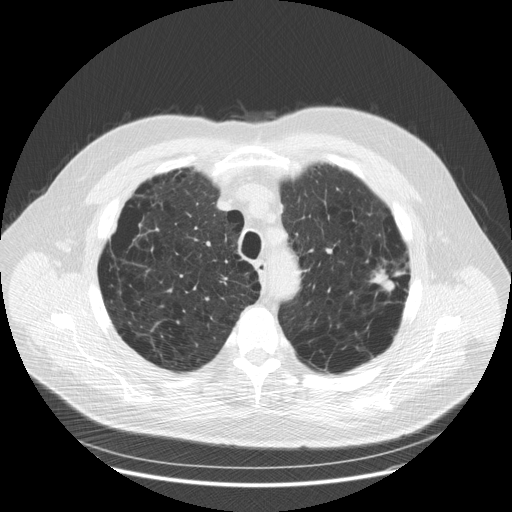
Low-dose screening chest CT, one axial slice; position 139 of 179 along the scan axis; 120 kVp; lung window (W 1500 / L -600 HU); 2.5 mm slice thickness; 512 × 512 image matrix, field of view 404 × 404 mm.
Structures marked on this image (expert manual segmentation):
- lesion 1 (tumor, upper lobe of left lung): bounding box (x1, y1, x2, y2) in pixels: (369, 268, 406, 292)